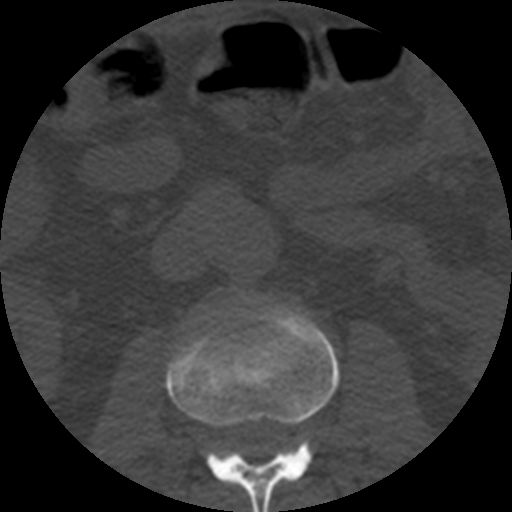
CT including the spine, one axial slice. Slice 145 of 508 in the series (ordered by position). Reconstruction kernel STANDARD. 120 kVp. Bone window (W 1800 / L 400 HU). 1.25 mm slice thickness. 512 × 512 image matrix. Patient age 57 years. From the clinical record (not read from this slice): primary cancer: prostate.
Annotated regions visible in this slice (semi-automatically segmented with operator editing):
- L2 vertebra: bounding box <165,300,339,512> (left, top, right, bottom; pixels)